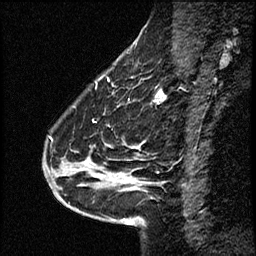
Breast MRI (dynamic contrast-enhanced), one sagittal slice. Position 19 of 50 along the scan axis. Dynamic contrast-enhanced study with each time point stored as its own series, time point 2 of 4 at this slice position (early post-contrast, ordered by acquisition time). 1.5 T. TE 4.2 ms, TR 17.5 ms. 3 mm slice thickness. 256 × 256 image matrix, field of view 200 × 200 mm. From the clinical record (not read from this slice): setting: breast cancer imaged before/during neoadjuvant chemotherapy.
Outlined on this slice (semi-automatic segmentation, software-assisted and operator-edited):
- analysis volume of interest (the breast-tissue region the enhancement analysis was run in; not a lesion): box from (x=52, y=99) to (x=158, y=207) px
- tumour enhancement mask (voxels above the 100 % enhancement threshold inside the analysis volume of interest): (x=85, y=101)–(x=158, y=180)